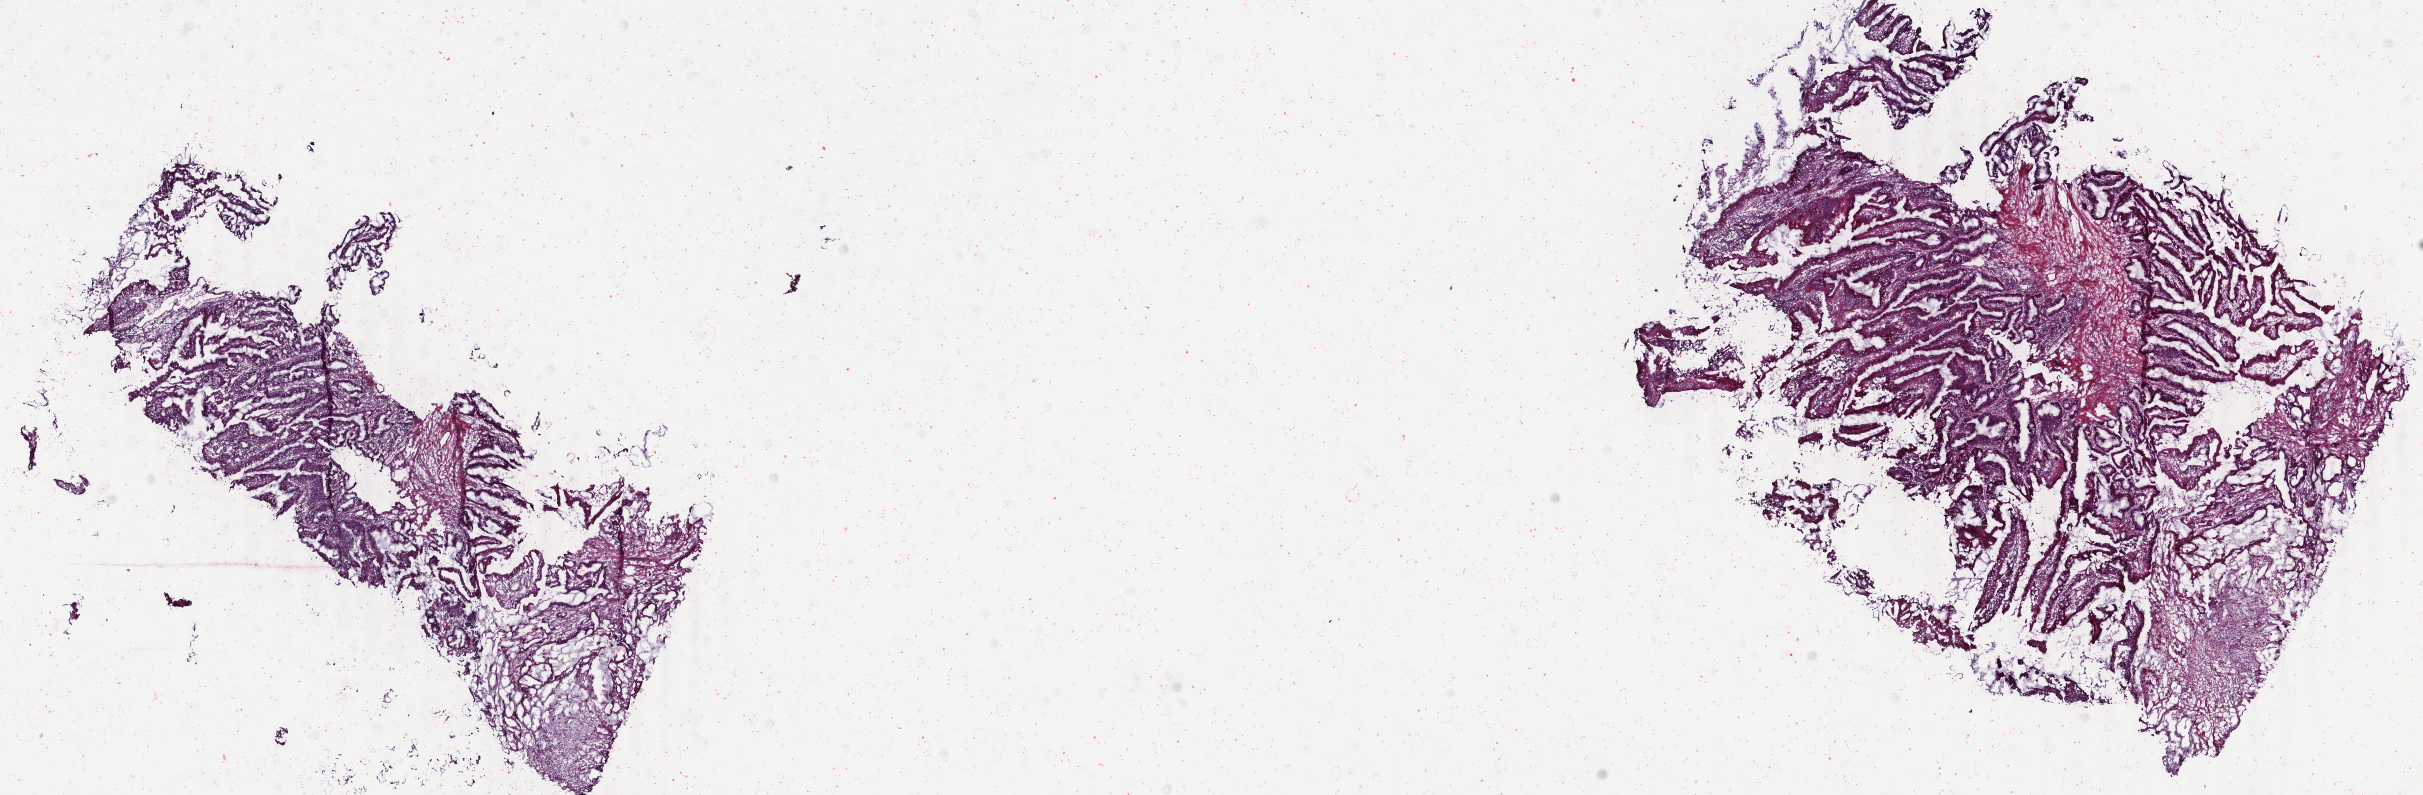
Hematoxylin and eosin (H&E) stained whole-slide image — a low-resolution overview of the entire scanned area, about 19.3 x 6.3 mm (slide scanned at 40x); frozen section; sample: primary tumour, colon. Female patient. Composition of this section per pathologist review: tumour cells 85%, tumour nuclei 75%, normal cells 0%, stromal cells 10%, necrosis 5%. Infiltration values recorded for this section: lymphocyte infiltration 15%, monocyte infiltration 1%, neutrophil infiltration 4%.
* histologic diagnosis: Mucinous adenocarcinoma
* TNM: T3 N2 M0
* AJCC pathologic stage: III
* lymph nodes positive (case pathology): 4 of 29 examined